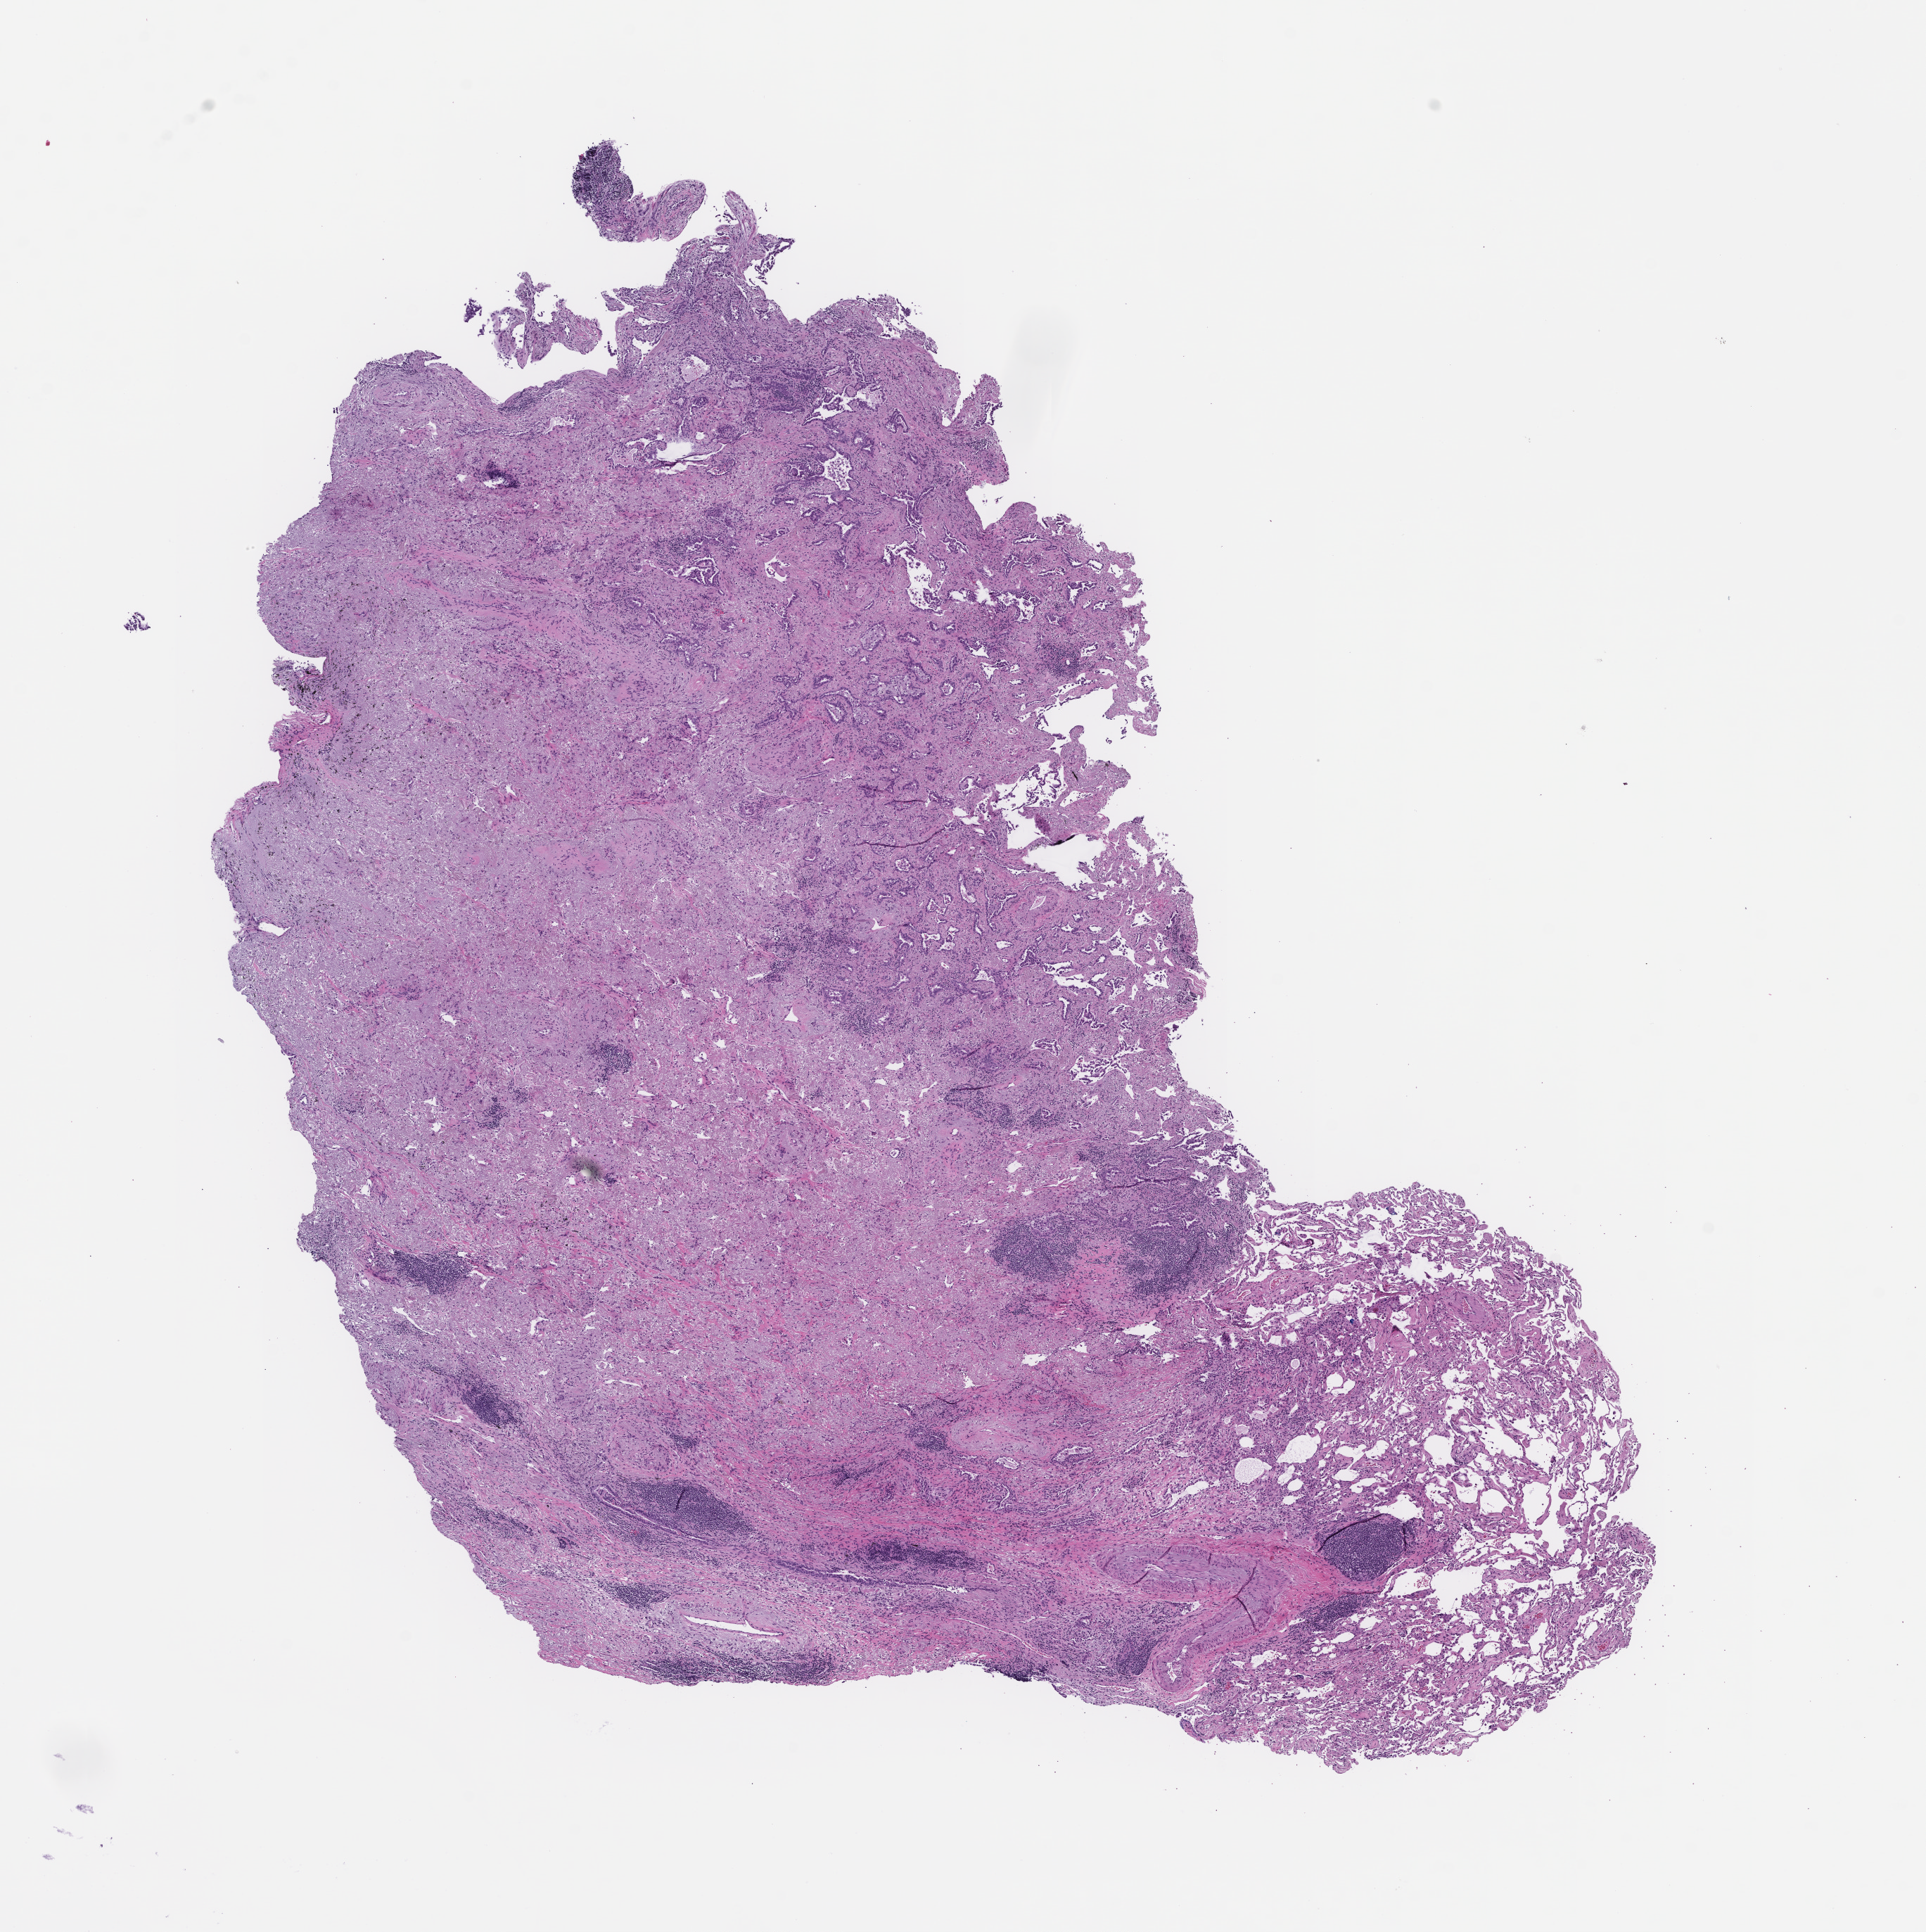
Haematoxylin and eosin whole-slide image, low-resolution overview of the scanned area, about 11.1 x 11.1 mm, formalin-fixed, paraffin-embedded (FFPE) tissue, site: lung, collected on treatment. Female patient.
This section: primary tumor. Diagnosis: Non-Small Cell Lung Carcinoma.